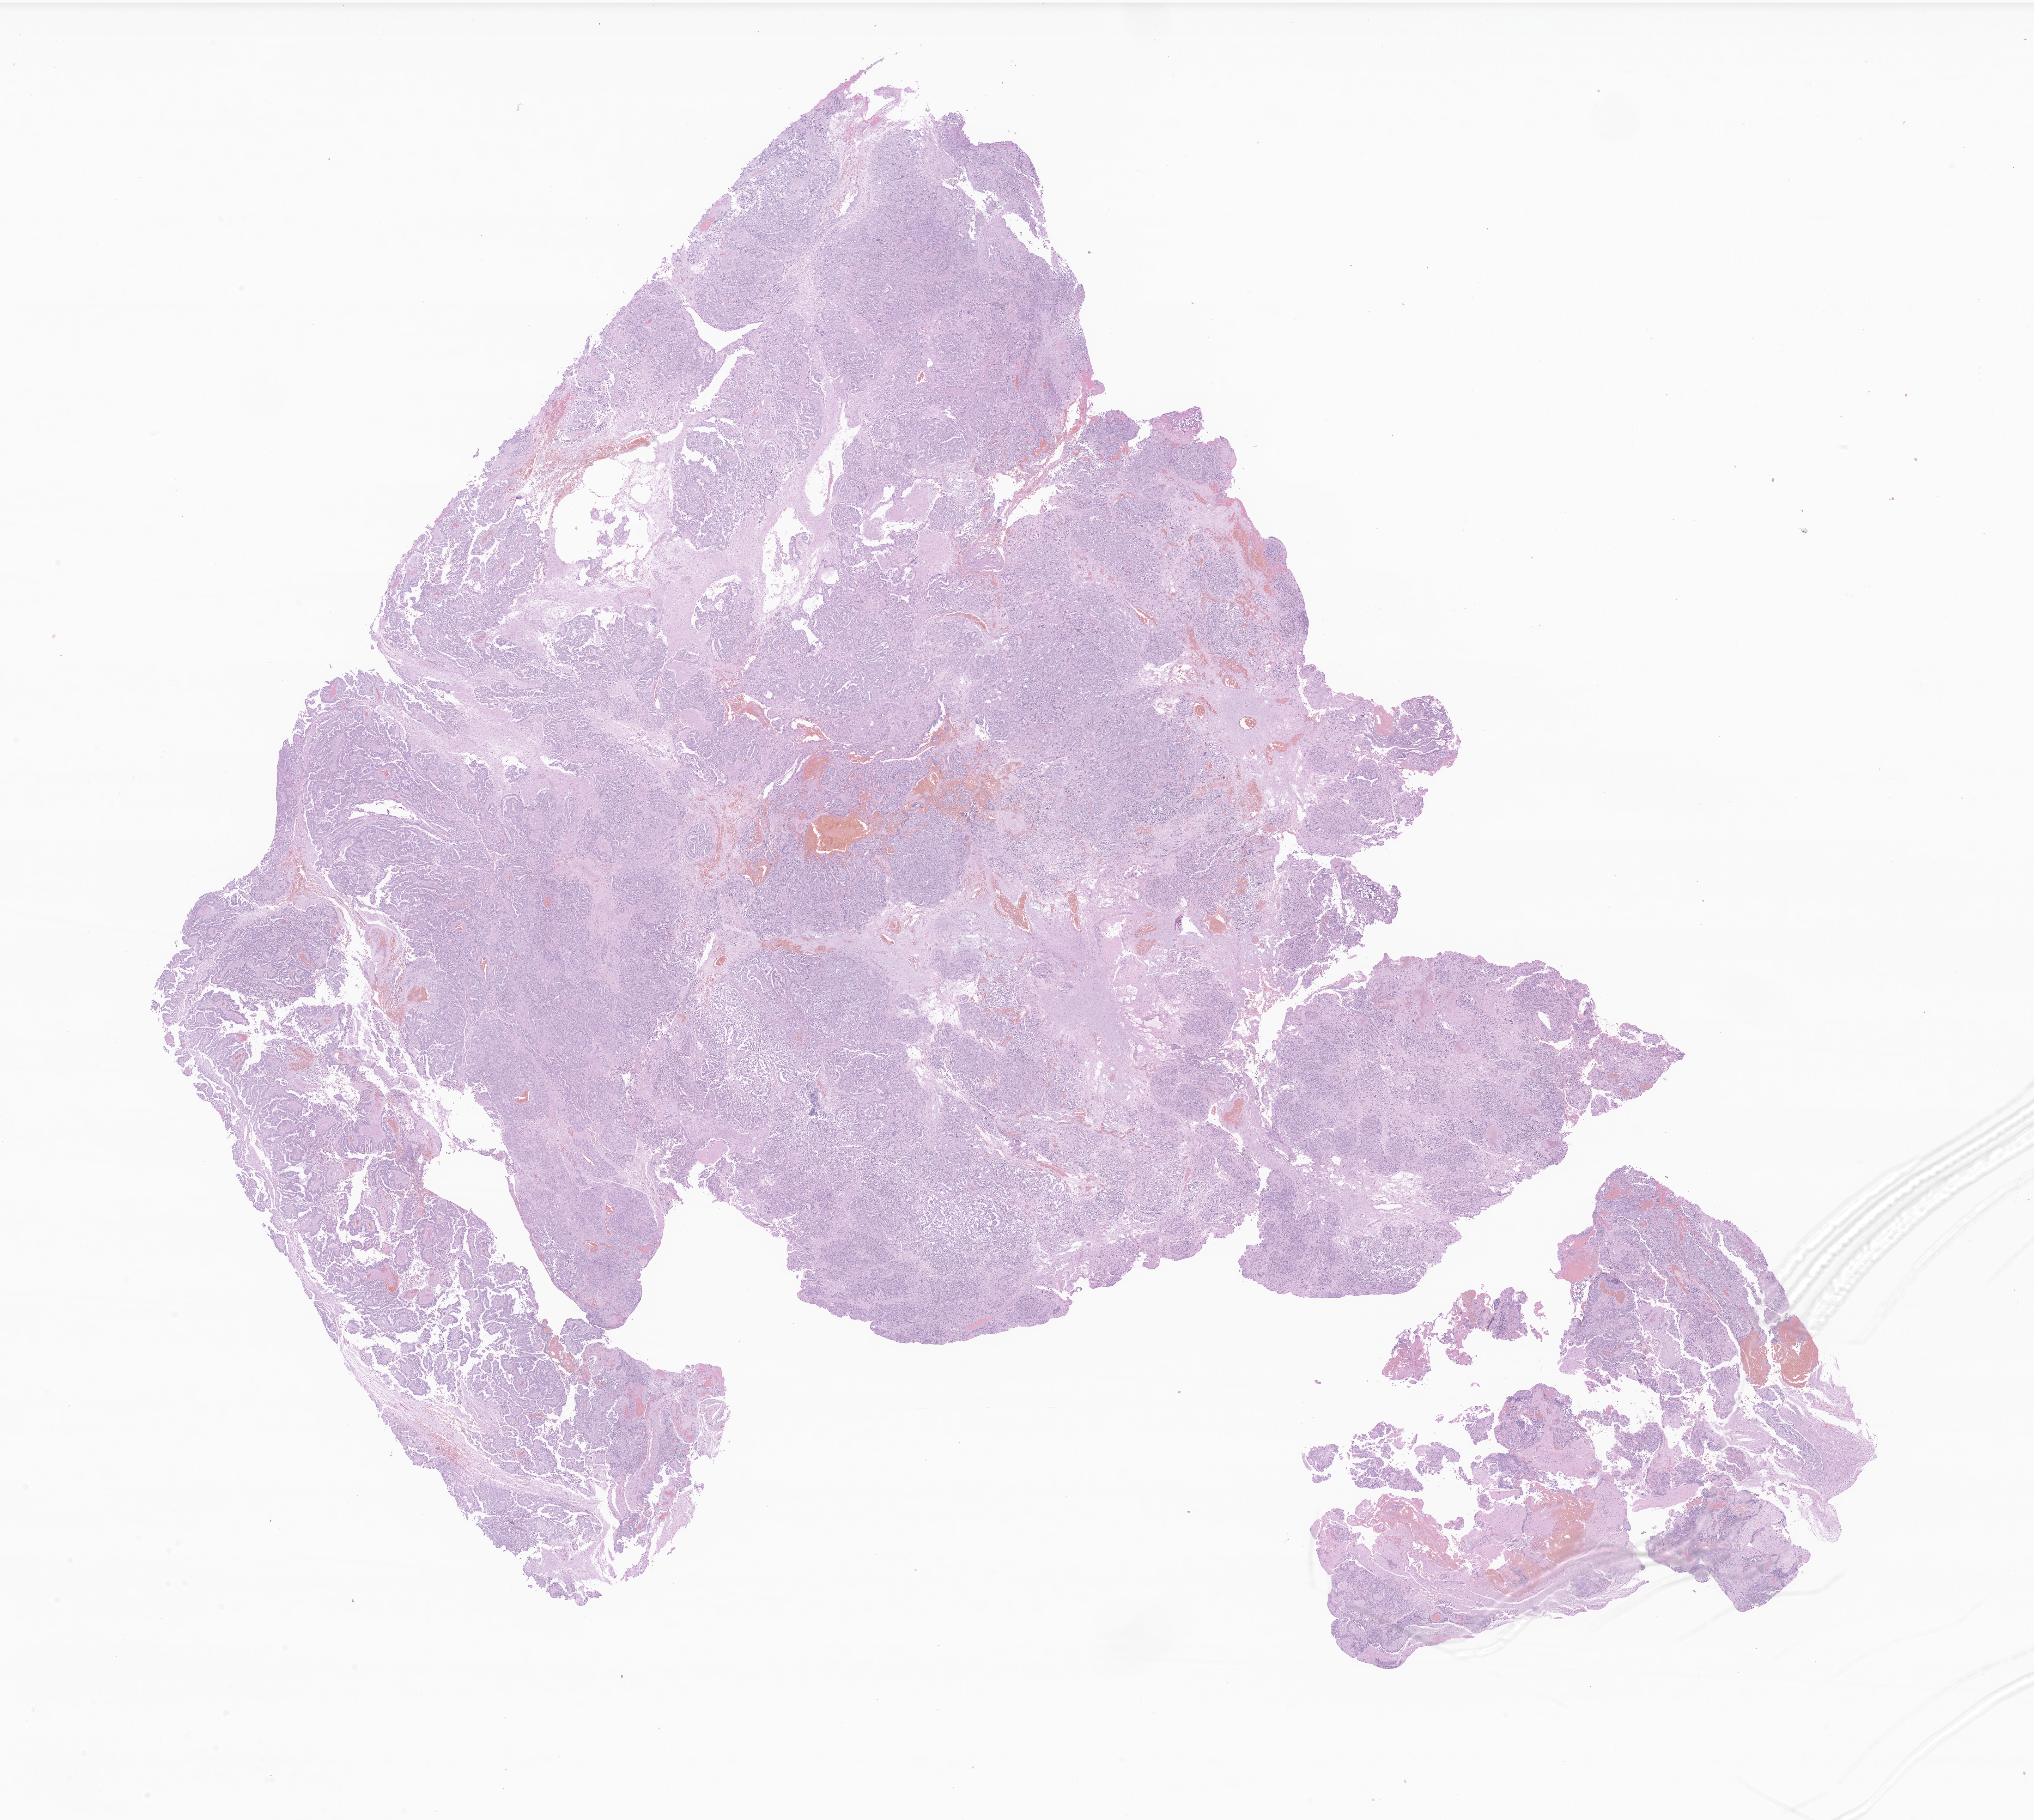
H&E whole-slide image of tumor tissue from the cerebrum, low-resolution overview of the scanned area, about 24.3 x 21.8 mm, formalin-fixed, paraffin-embedded (FFPE) tissue. Female patient, age 34 months (2 years 10 months).
- diagnosis (ICD-O-3 morphology term): Choroid plexus carcinoma